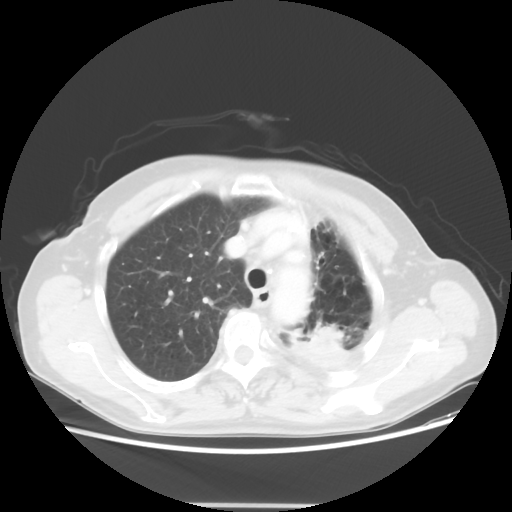
Chest CT, one axial slice. Slice 41 of 56 in the series (ordered by position). Reconstruction kernel STANDARD. 100 kVp. Lung window (W 1500 / L -600 HU). 5 mm slice thickness. 512 × 512 image matrix. Female patient, age 63 years. Case-level facts recorded for this patient, not image findings: clinical TNM (as recorded): T2a N0 M0.
Annotated regions visible in this slice (rectangle marked by the reading radiologist):
- lung tumour (recorded histology: adenocarcinoma): bounding box <306,323,345,362> (left, top, right, bottom; pixels)